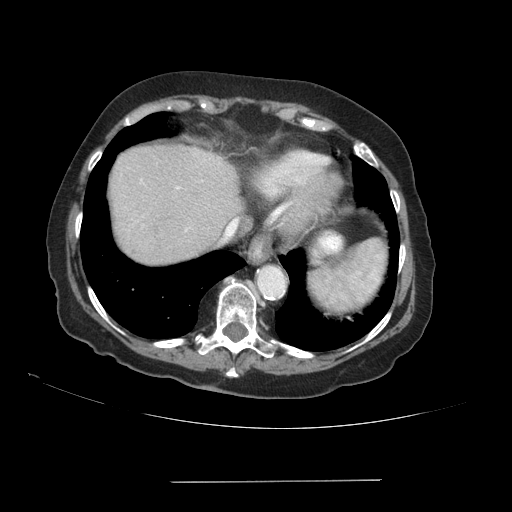
Contrast-enhanced abdominal CT (liver protocol), one axial slice; position 77 of 89 along the scan axis; 140 kVp; soft-tissue window (W 400 / L 40 HU); 2.5 mm slice thickness; 512 × 512 image matrix, field of view 400 × 400 mm. From the clinical record (not read from this slice): diagnosis: hepatocellular carcinoma (patient treated with transarterial chemoembolisation; whether this scan precedes or follows treatment is not stated here); TNM stage (as recorded): Stage-IVA; Child-Pugh class: A; tumour differentiation: poorly differentiated.
Annotated regions visible in this slice (semi-automatically segmented with operator editing):
- liver parenchyma outside the tumour (the mass and vessels are separate outlines, so this box may not span the whole liver): bounding box <108,146,241,264> (left, top, right, bottom; pixels)